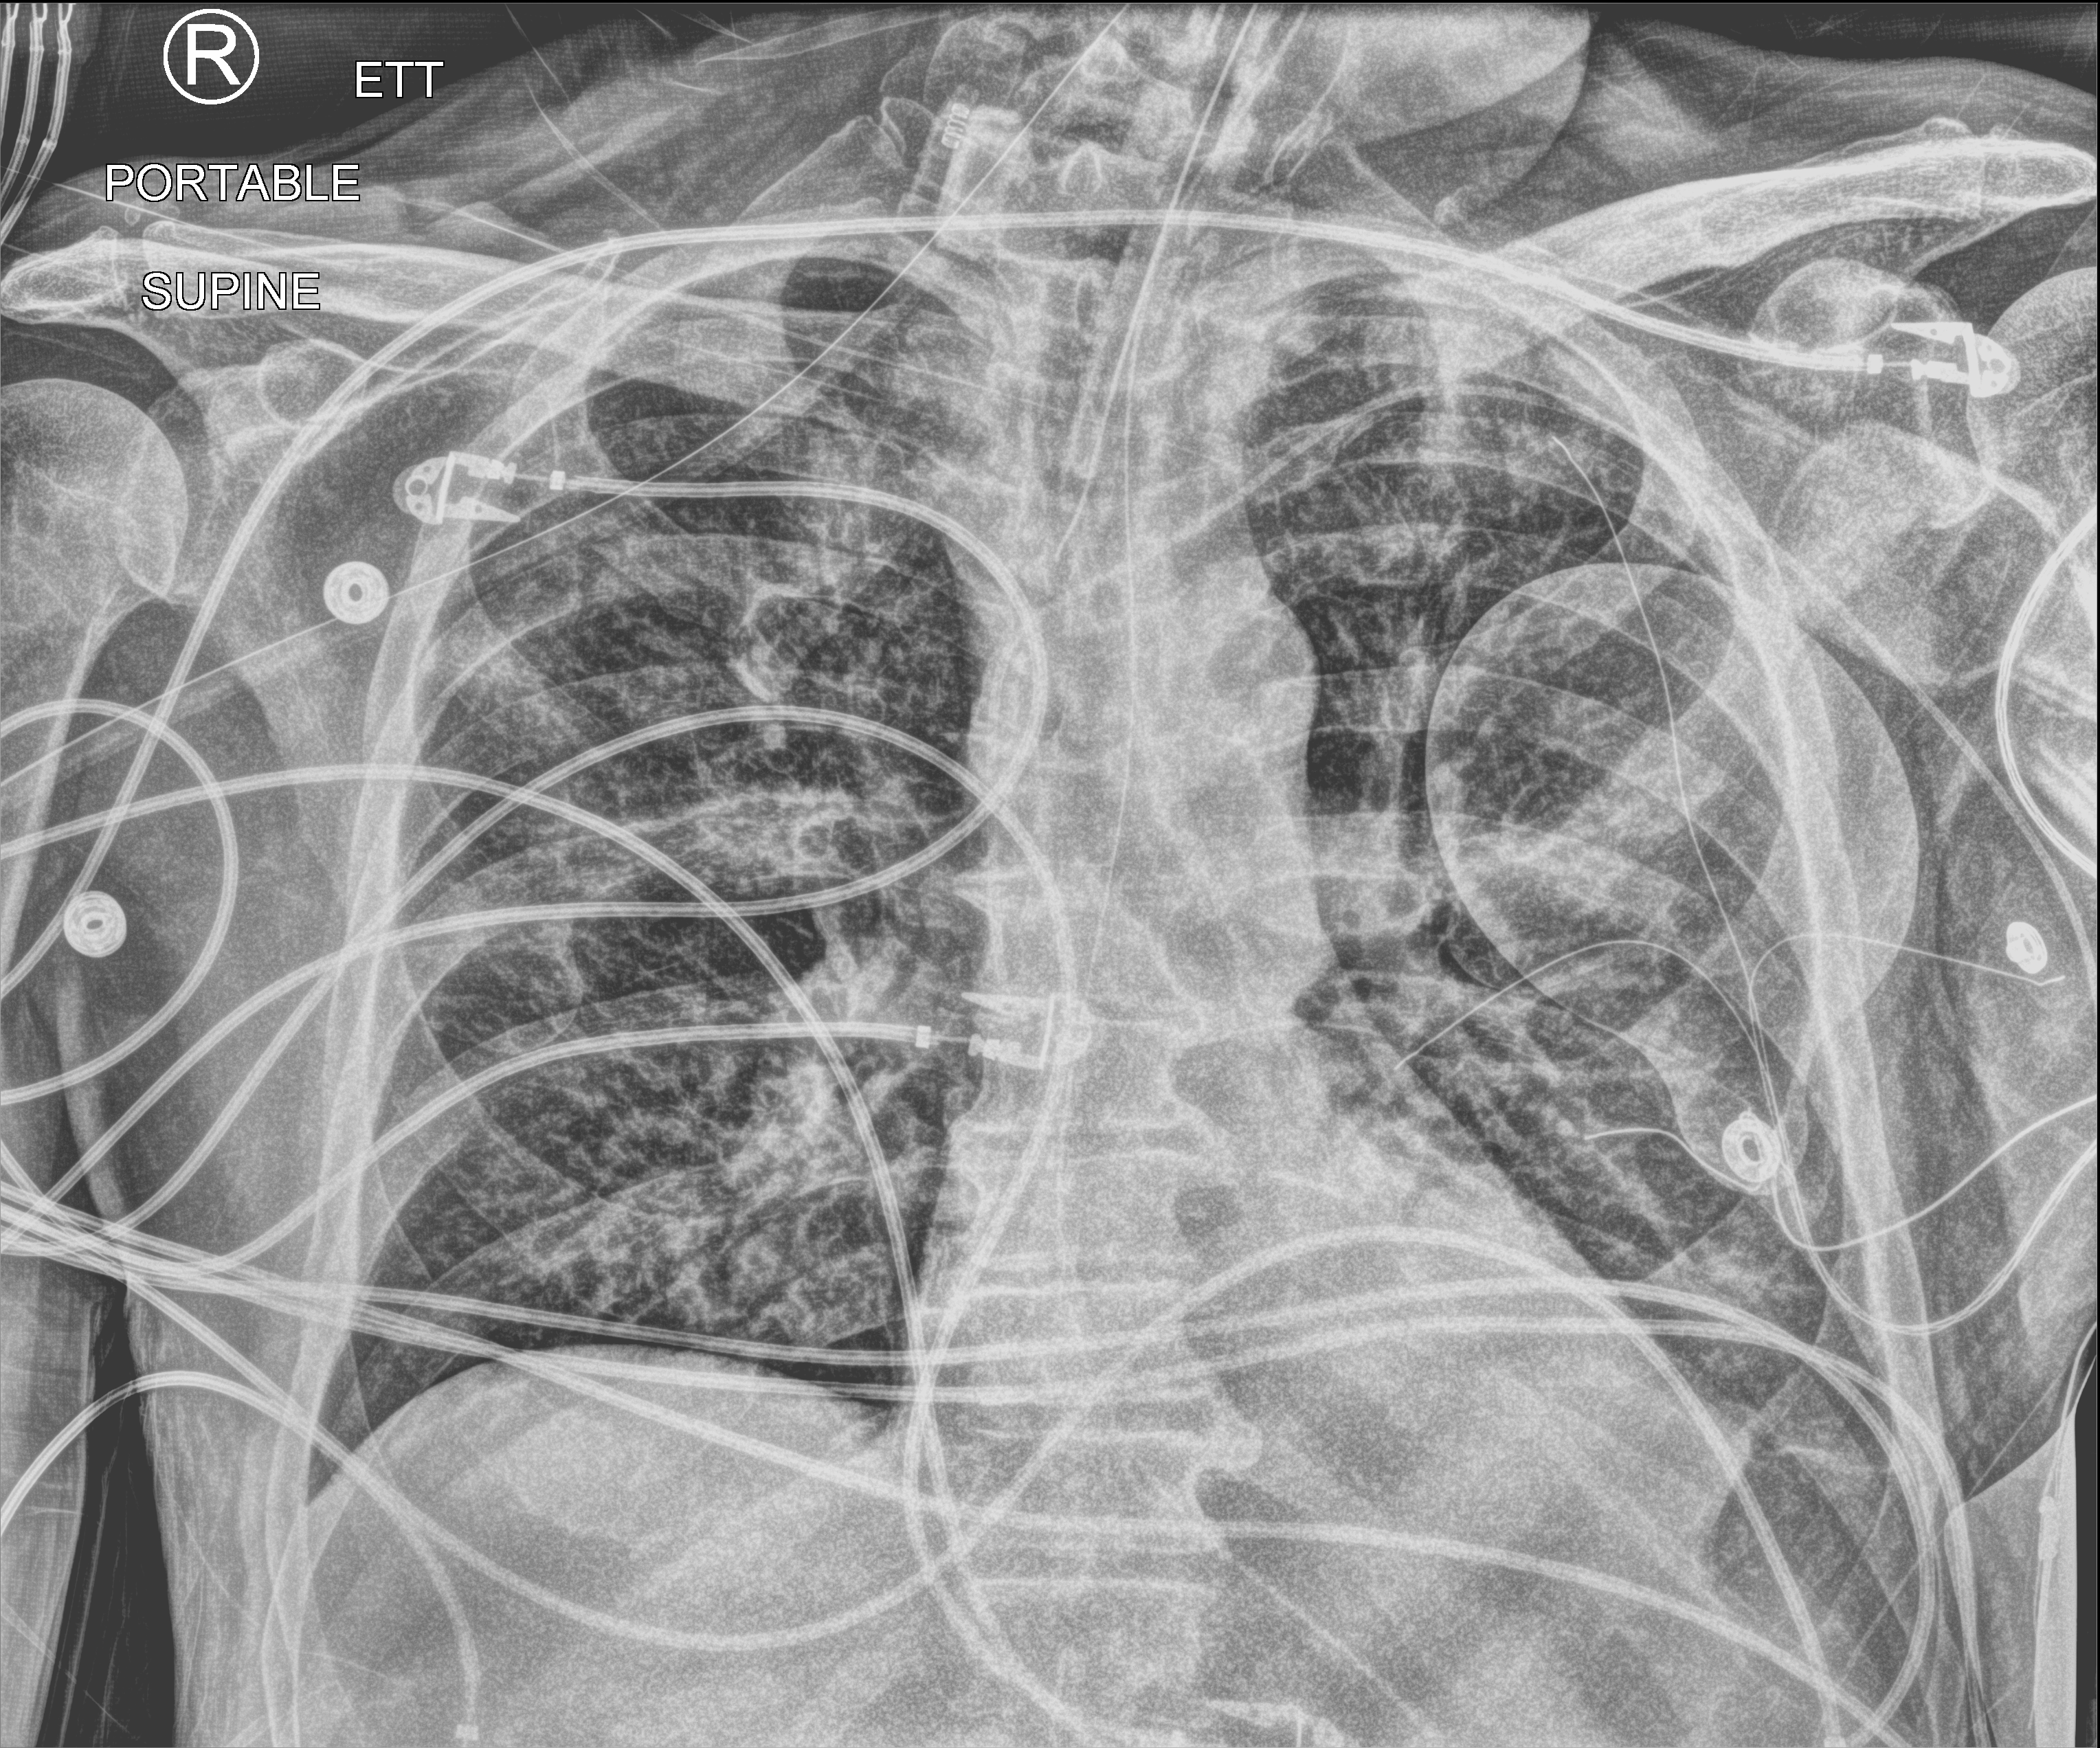
Bedside chest radiograph (computed radiography); anteroposterior (AP) projection. Male patient hospitalised with COVID-19, age 60–74 years.
Hospital-stay facts (about this admission, not read from this image; timing relative to this image not recorded):
- length of hospital stay: 35 days
- mechanically ventilated during this hospital stay: yes
- admitted to intensive care during this hospital stay: yes